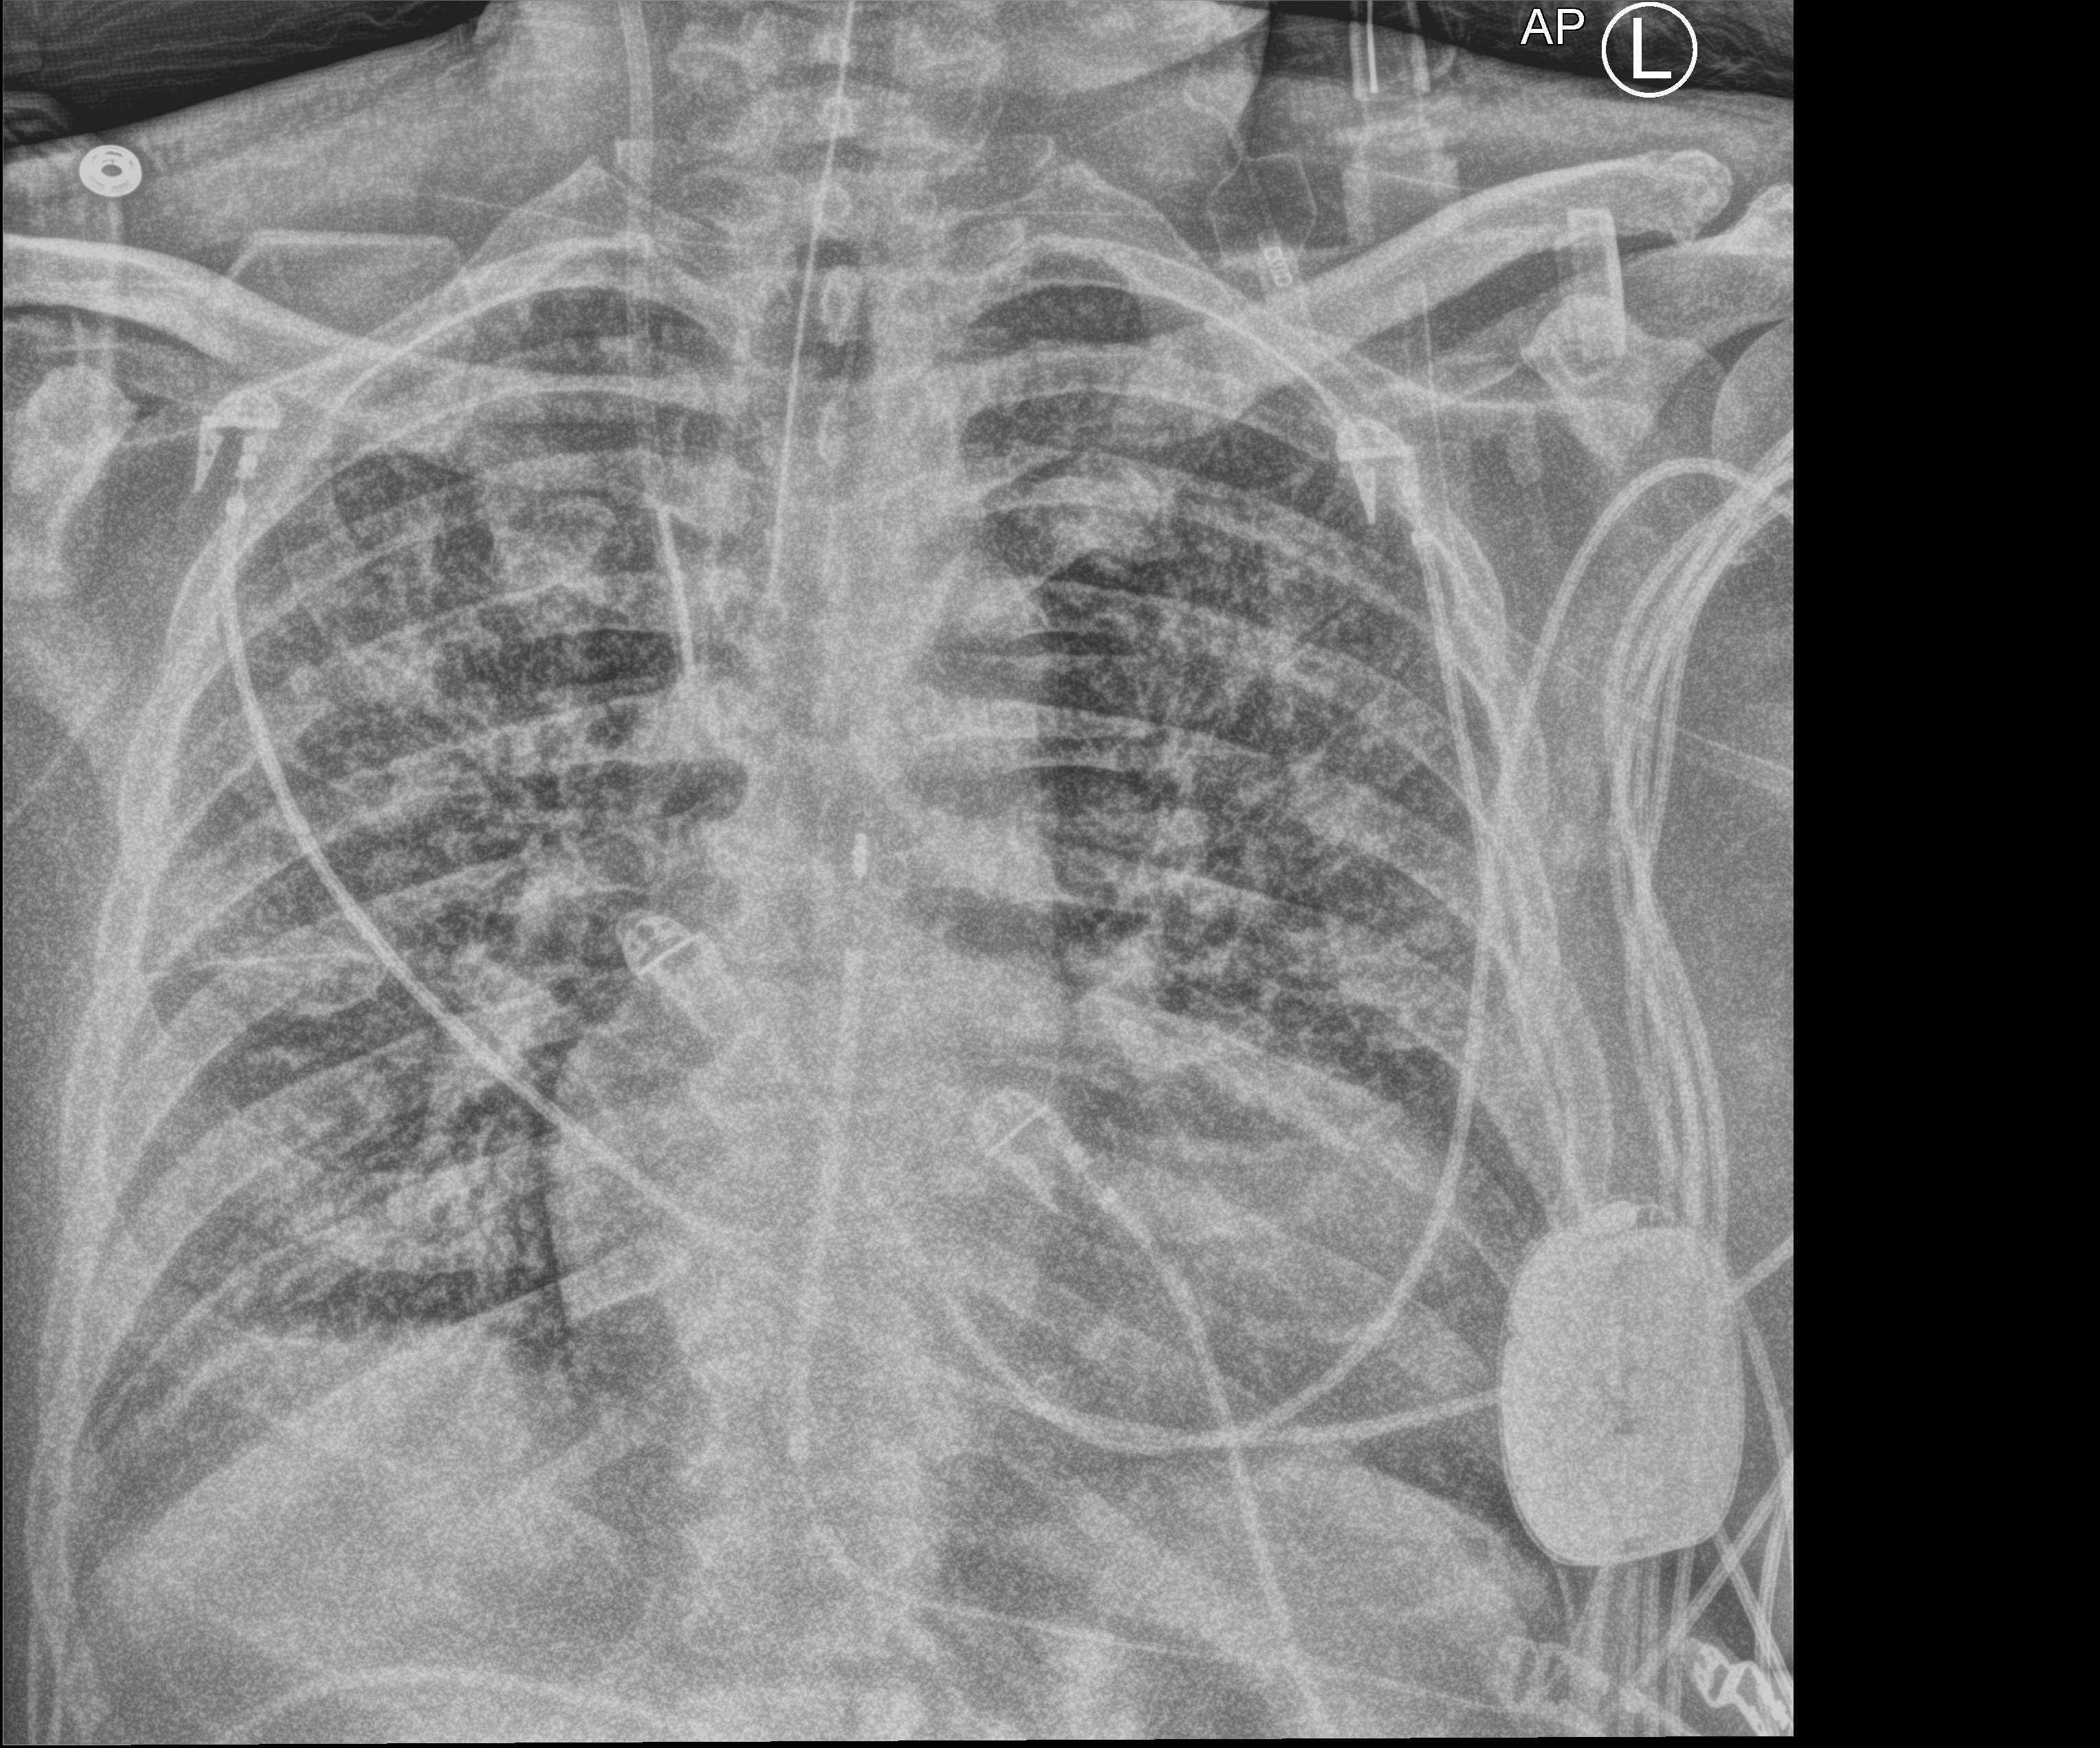
Chest X-ray (portable). Patient hospitalised with COVID-19; male, aged 60–74 years.
Admission-level facts for this patient (not findings on this image; timing relative to this image not recorded): mechanically ventilated during this hospital stay: yes; chronic kidney disease (admission record): no; admitted to intensive care during this hospital stay: yes.